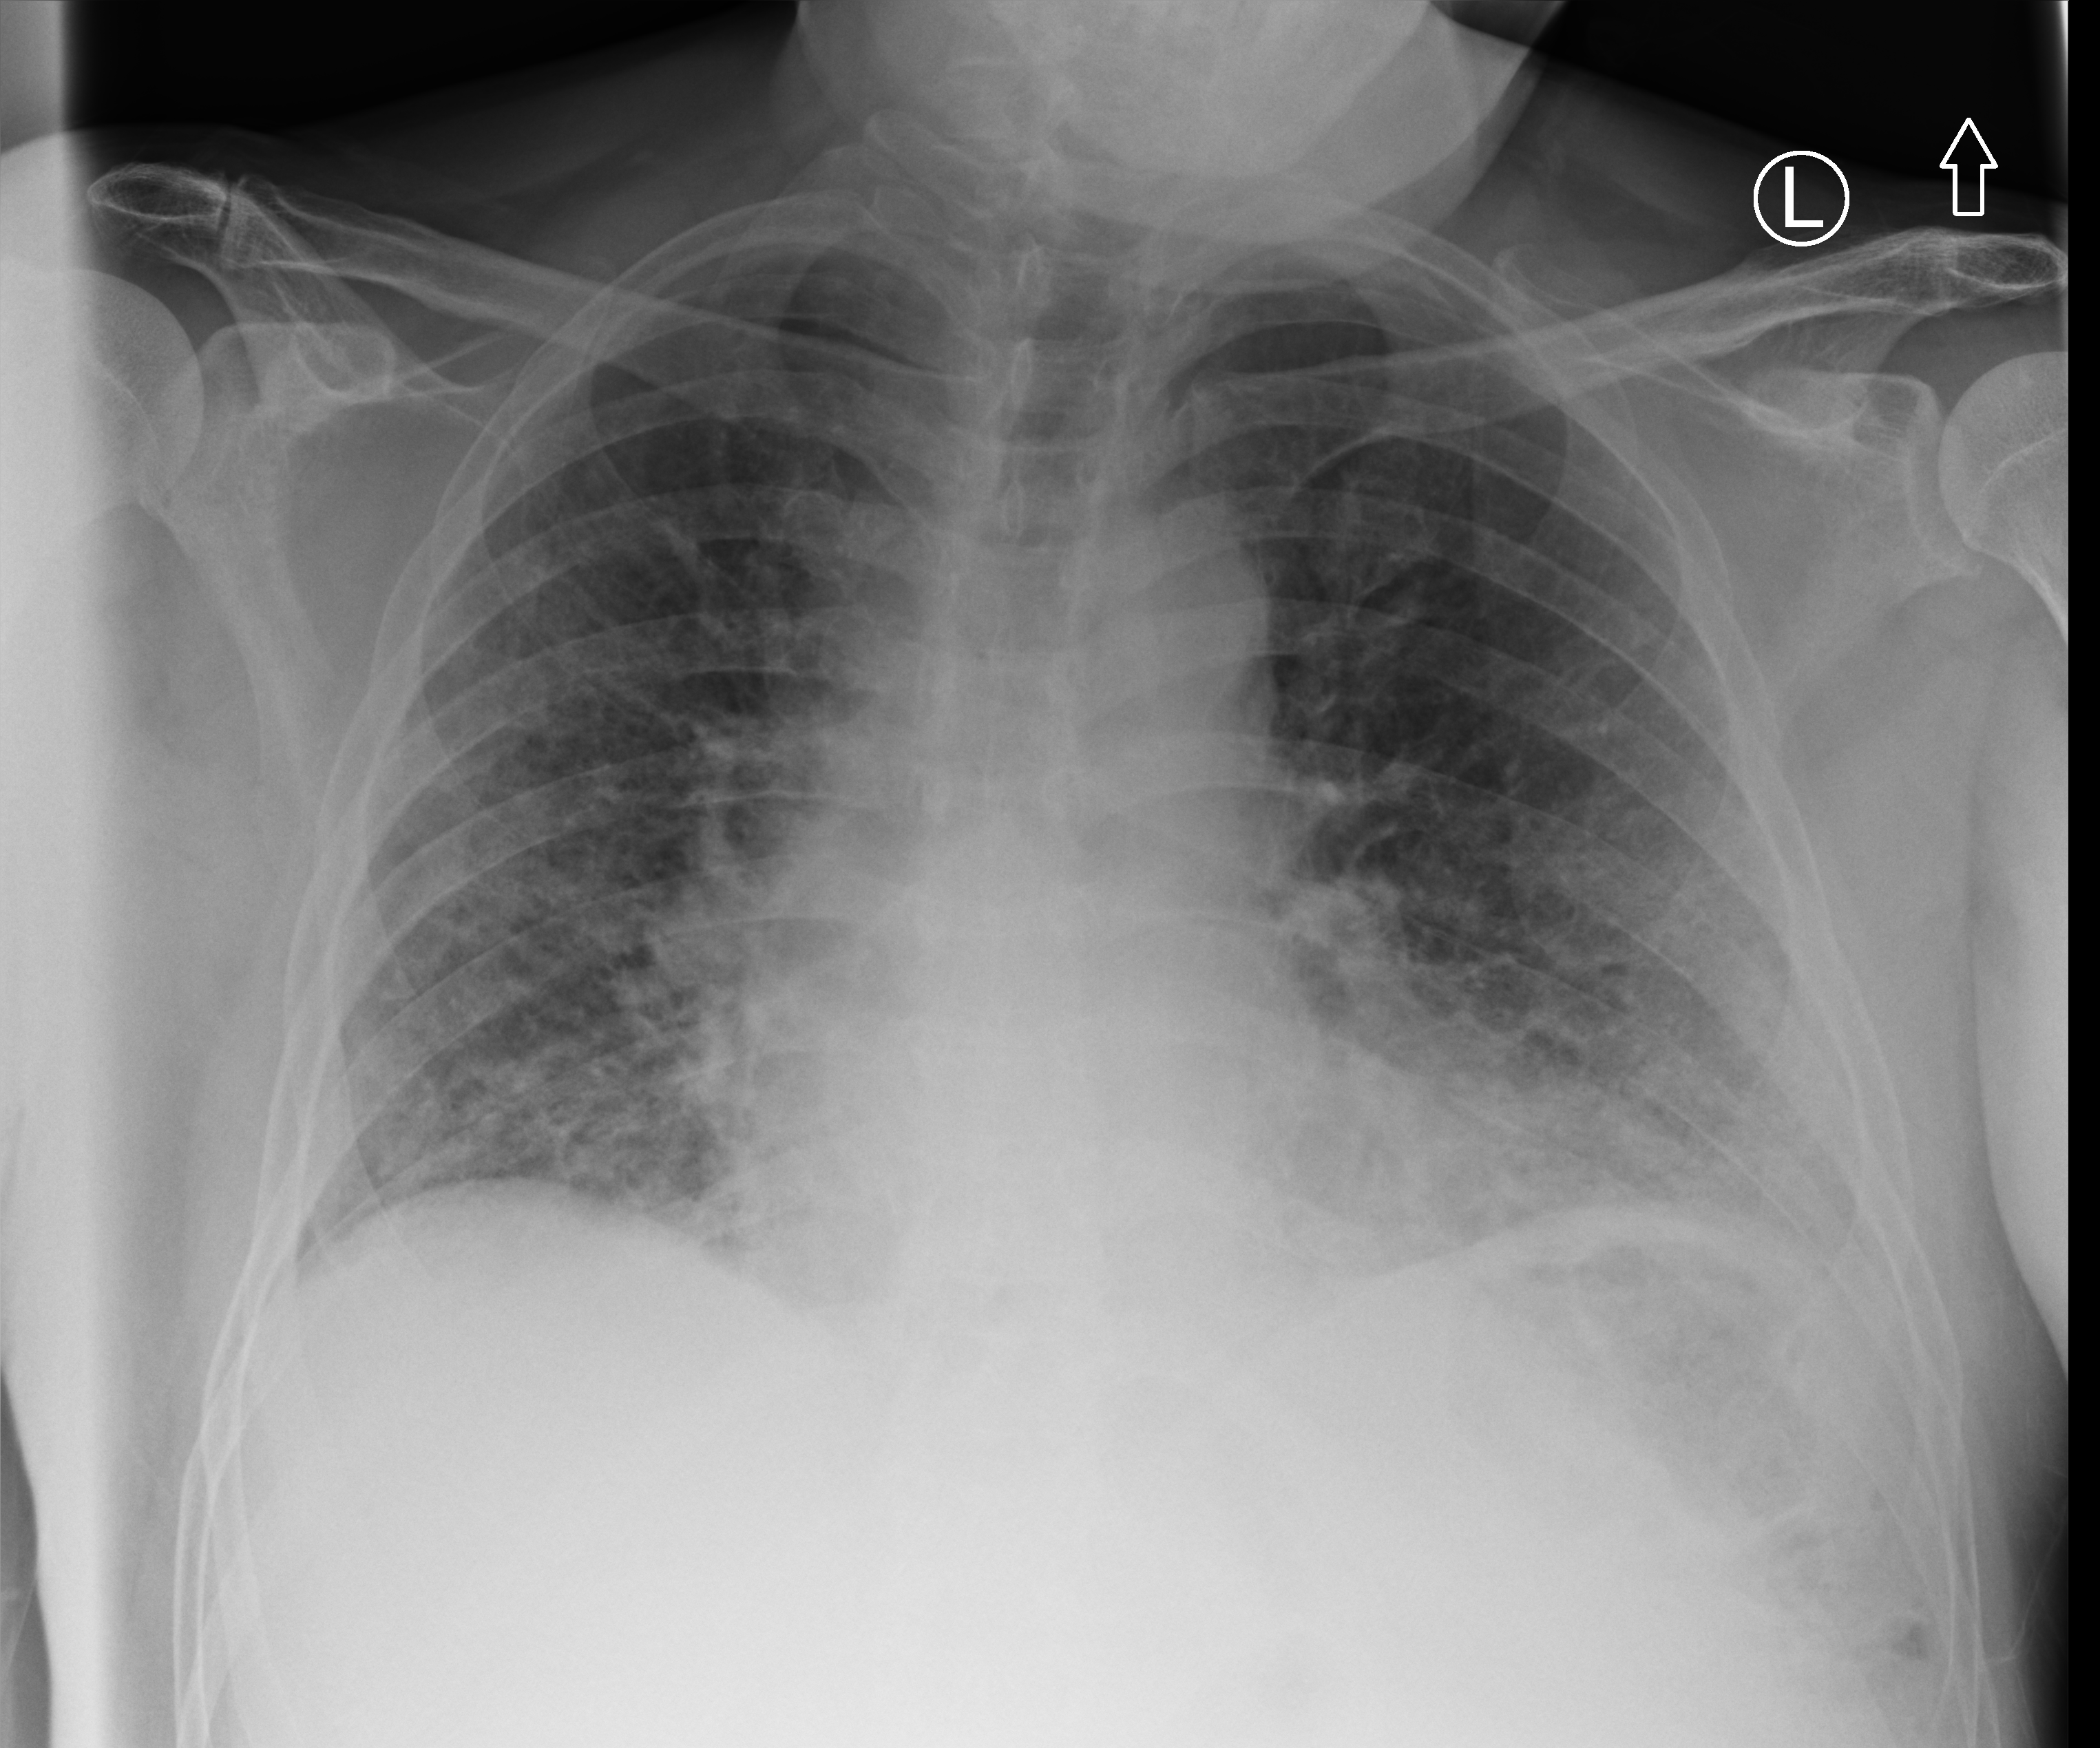
Portable chest radiograph, anteroposterior (AP) projection. Patient hospitalised with COVID-19; male, aged 60–74 years.
Hospital-stay facts (about this admission, not read from this image; timing relative to this image not recorded): length of hospital stay: 54 days; mechanically ventilated during this hospital stay: yes.